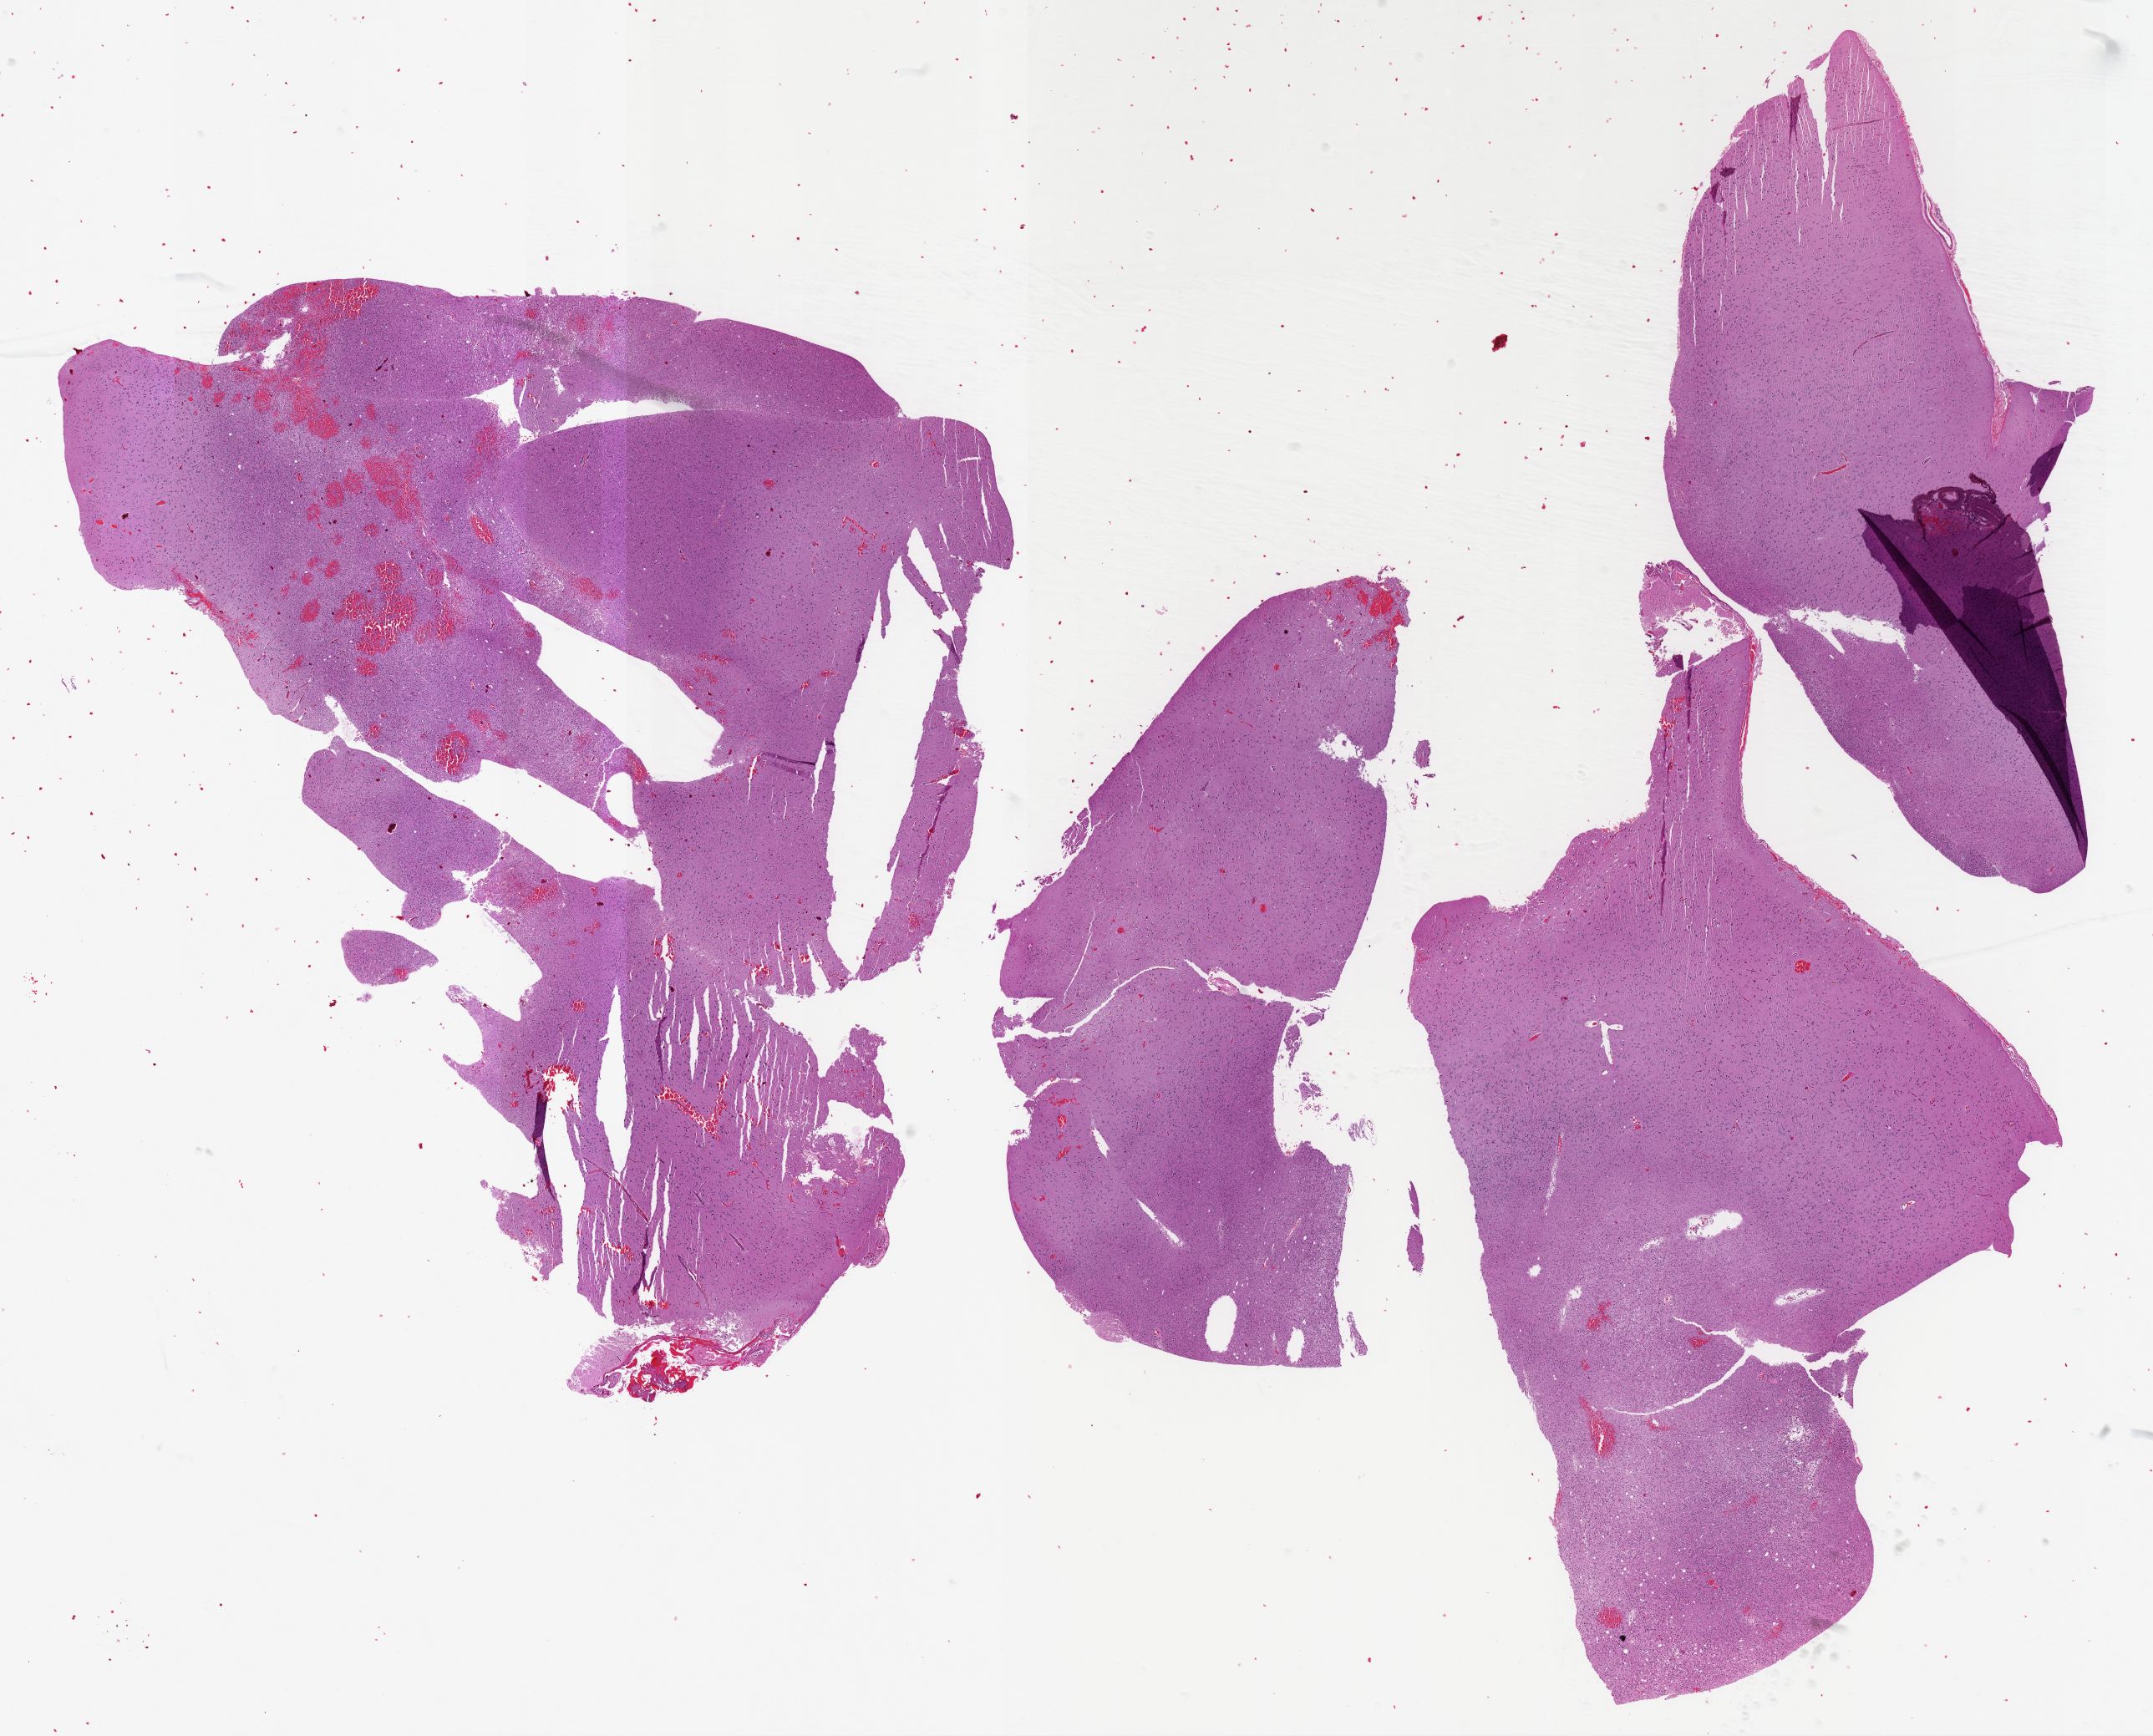
Hematoxylin and eosin (H&E) stained whole-slide image — shown as a low-resolution overview of the whole scanned area (about 20.8 x 16.8 mm); formalin-fixed paraffin-embedded (FFPE) diagnostic section; sample: primary tumour, brain. Male, age 31 years at initial diagnosis. Histologic grade: G2 (moderately differentiated).
Pathologic diagnosis: Oligodendroglioma, NOS (cerebrum).